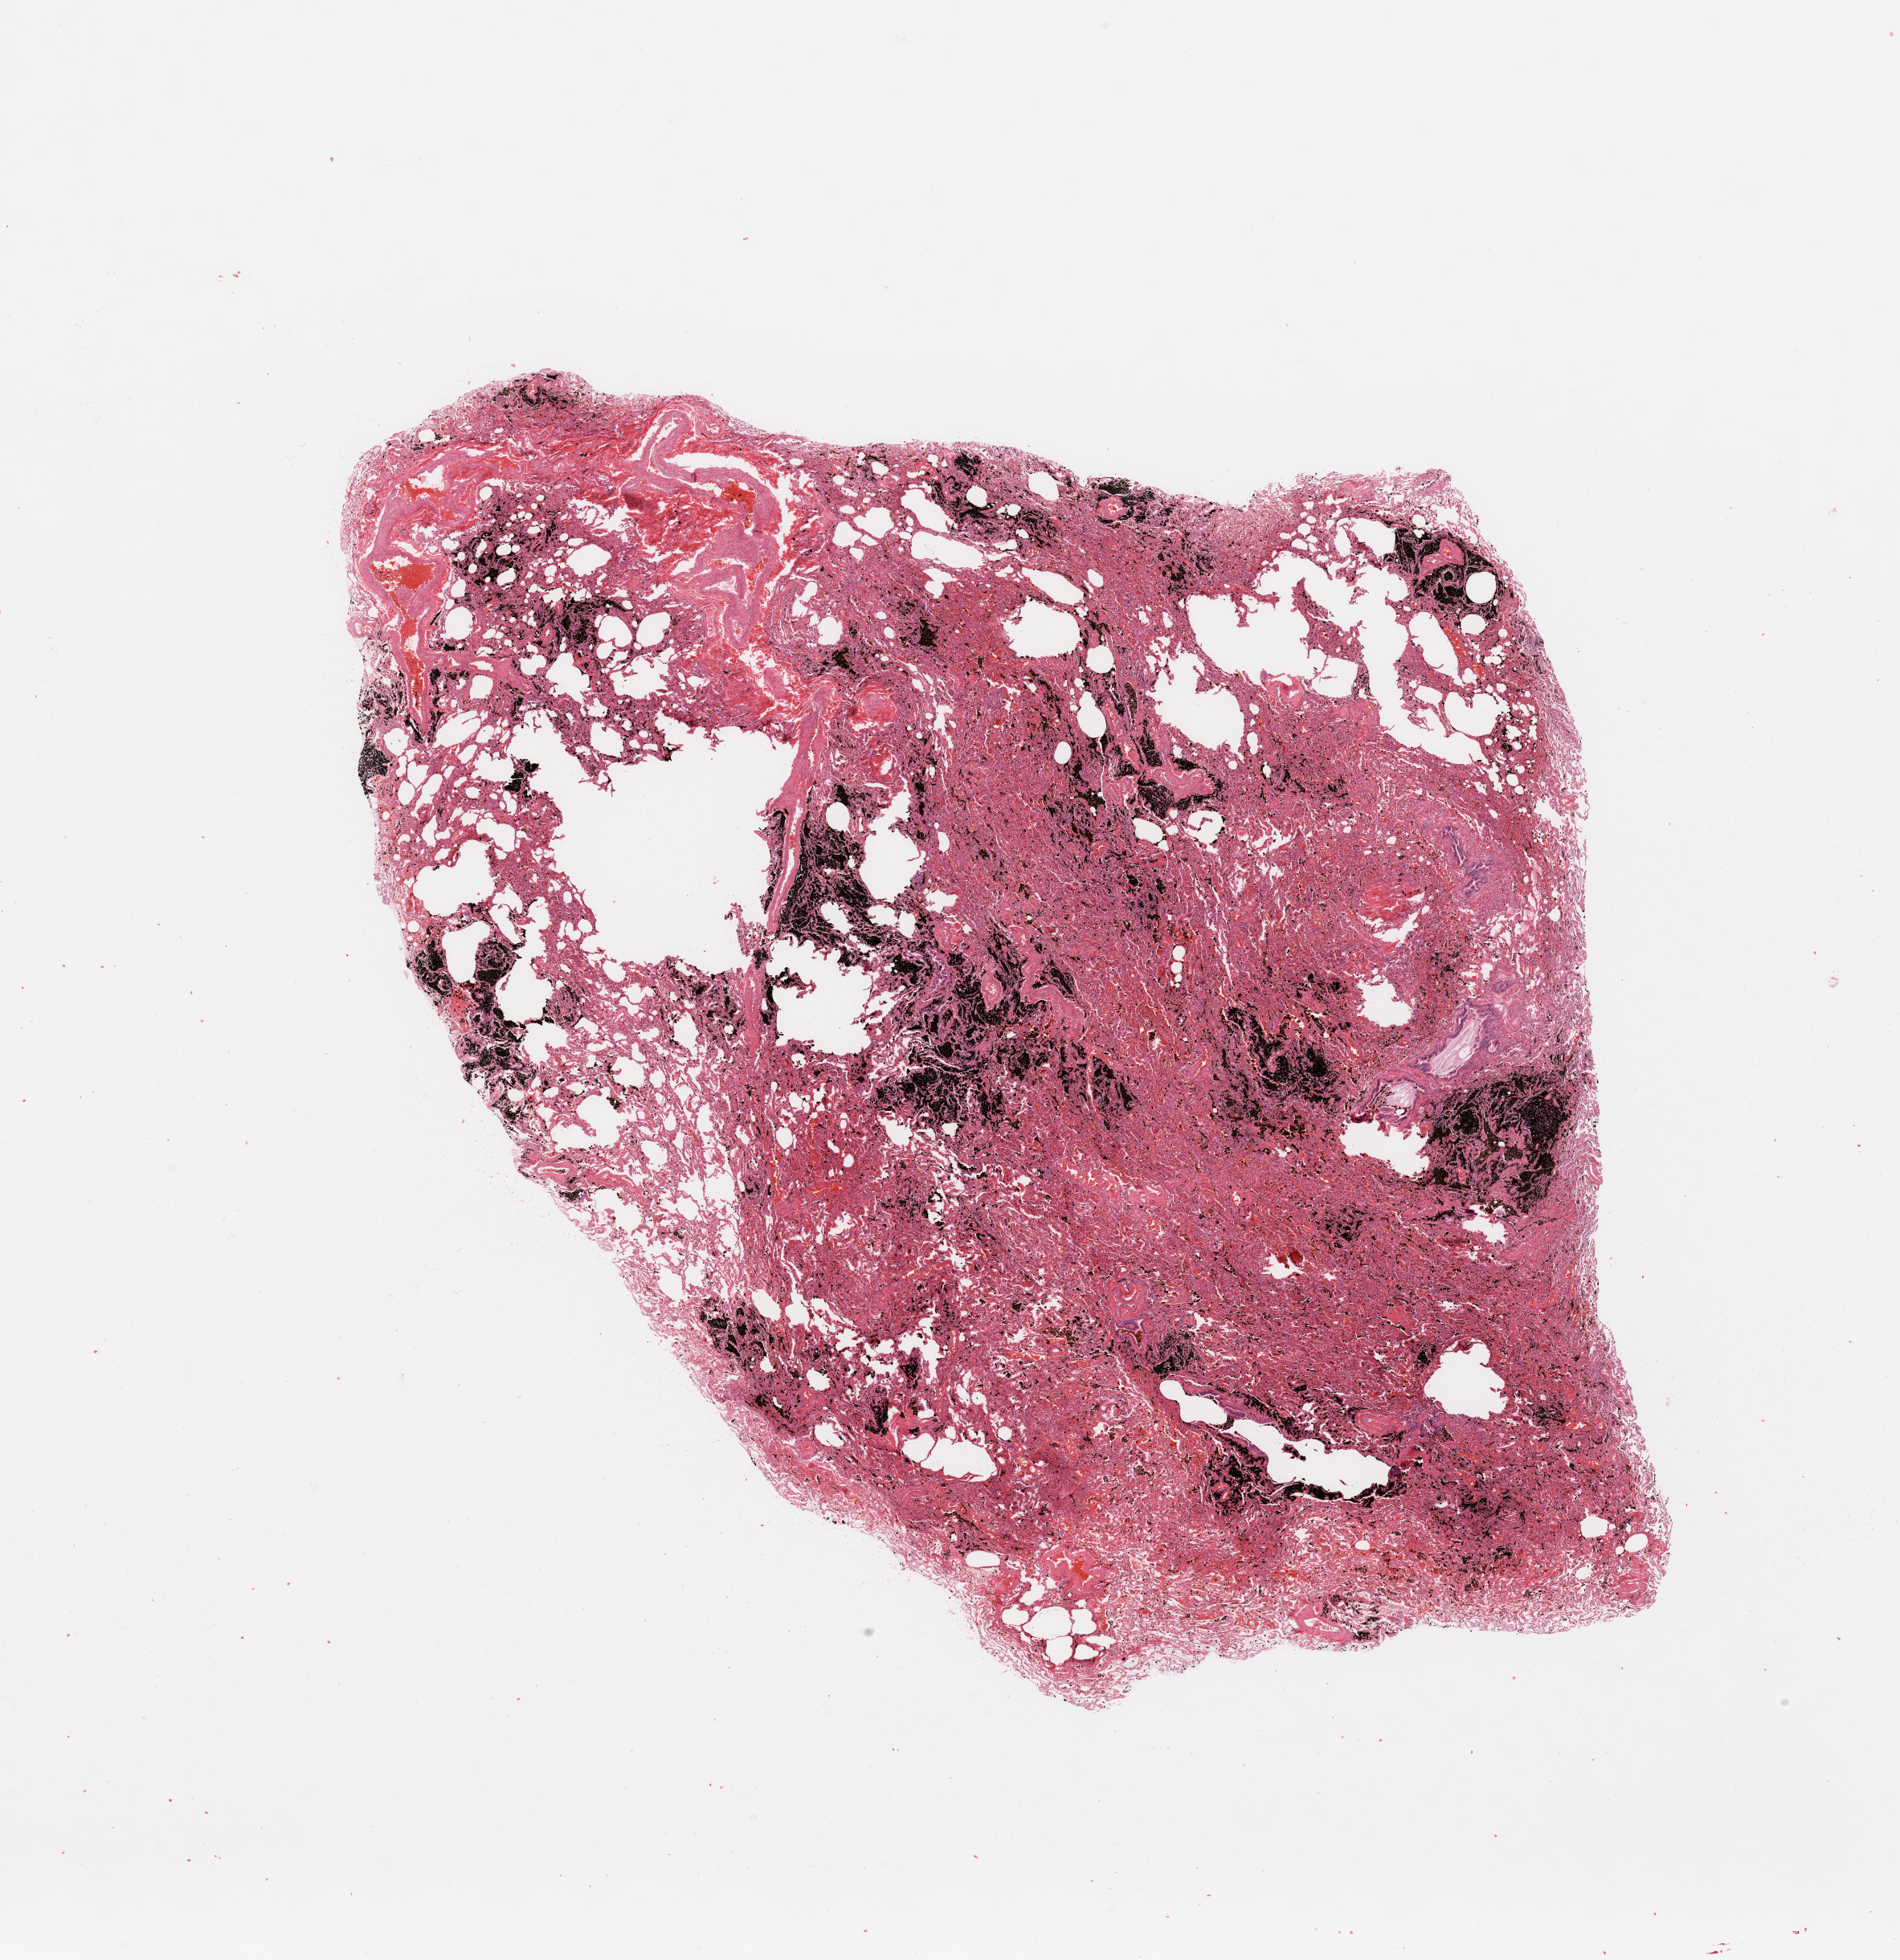
Whole-slide histology image, H&E-stained, low-resolution overview of the scanned area, about 18.7 x 19.3 mm; normal (non-tumour) tissue sample, sampled site: lung. 56-year-old male patient.
* this section: normal (non-tumour) tissue from the same patient
* patient diagnosis: Adenocarcinoma, NOS